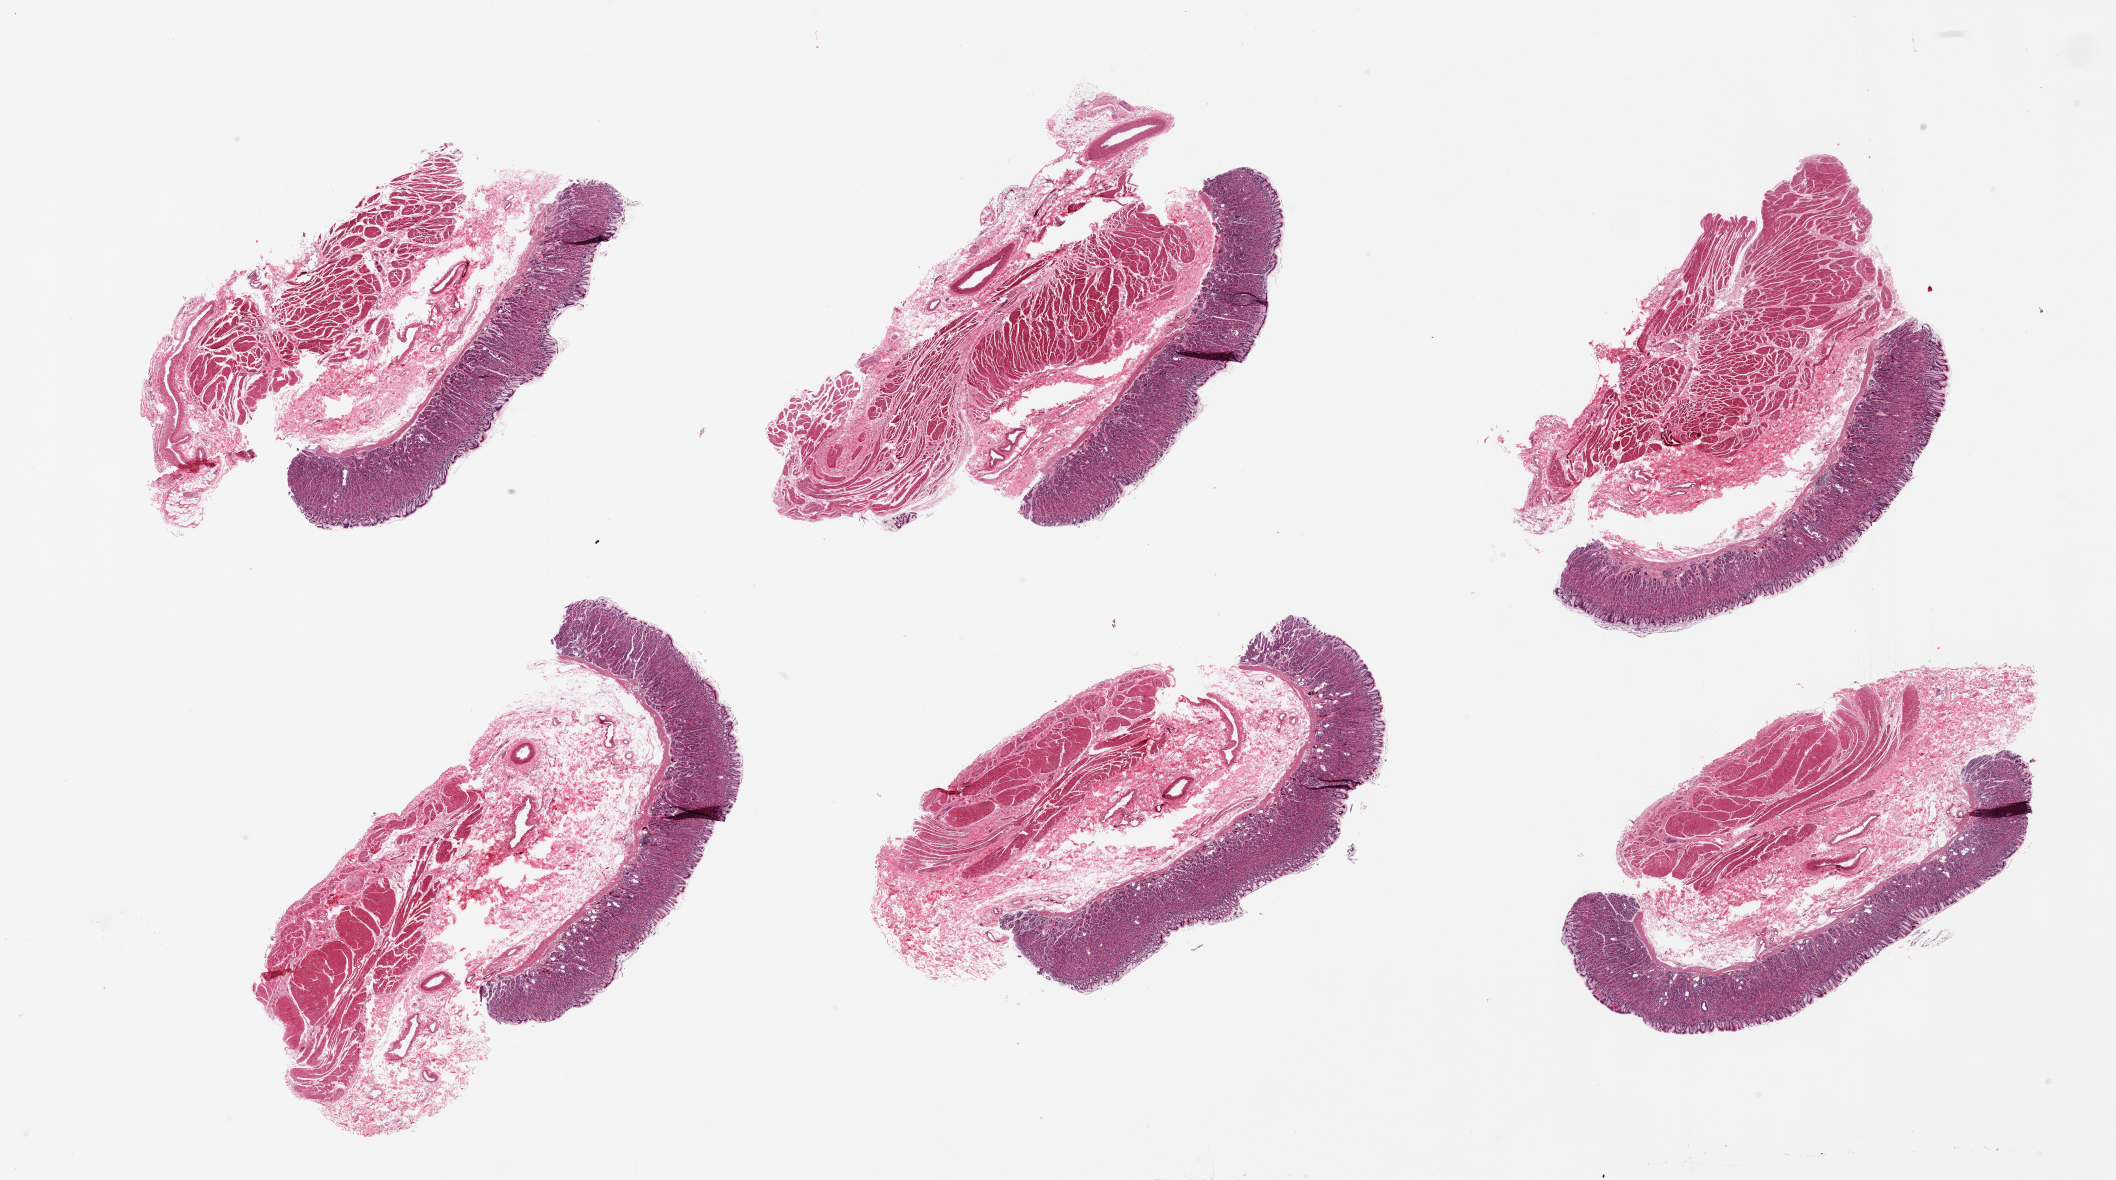
H&E whole-slide image, brightfield — shown as a low-resolution overview of the whole scanned area (about 33.5 x 18.7 mm, from a 20x scan); PAXgene-fixed paraffin-embedded (PFPE) section; section of stomach (target tissue); tissue donor sample. Male donor.
Pathologist's review note for this sample: 6 pieces; full thickness sections, several larger vessels attached, dilated deep glands.